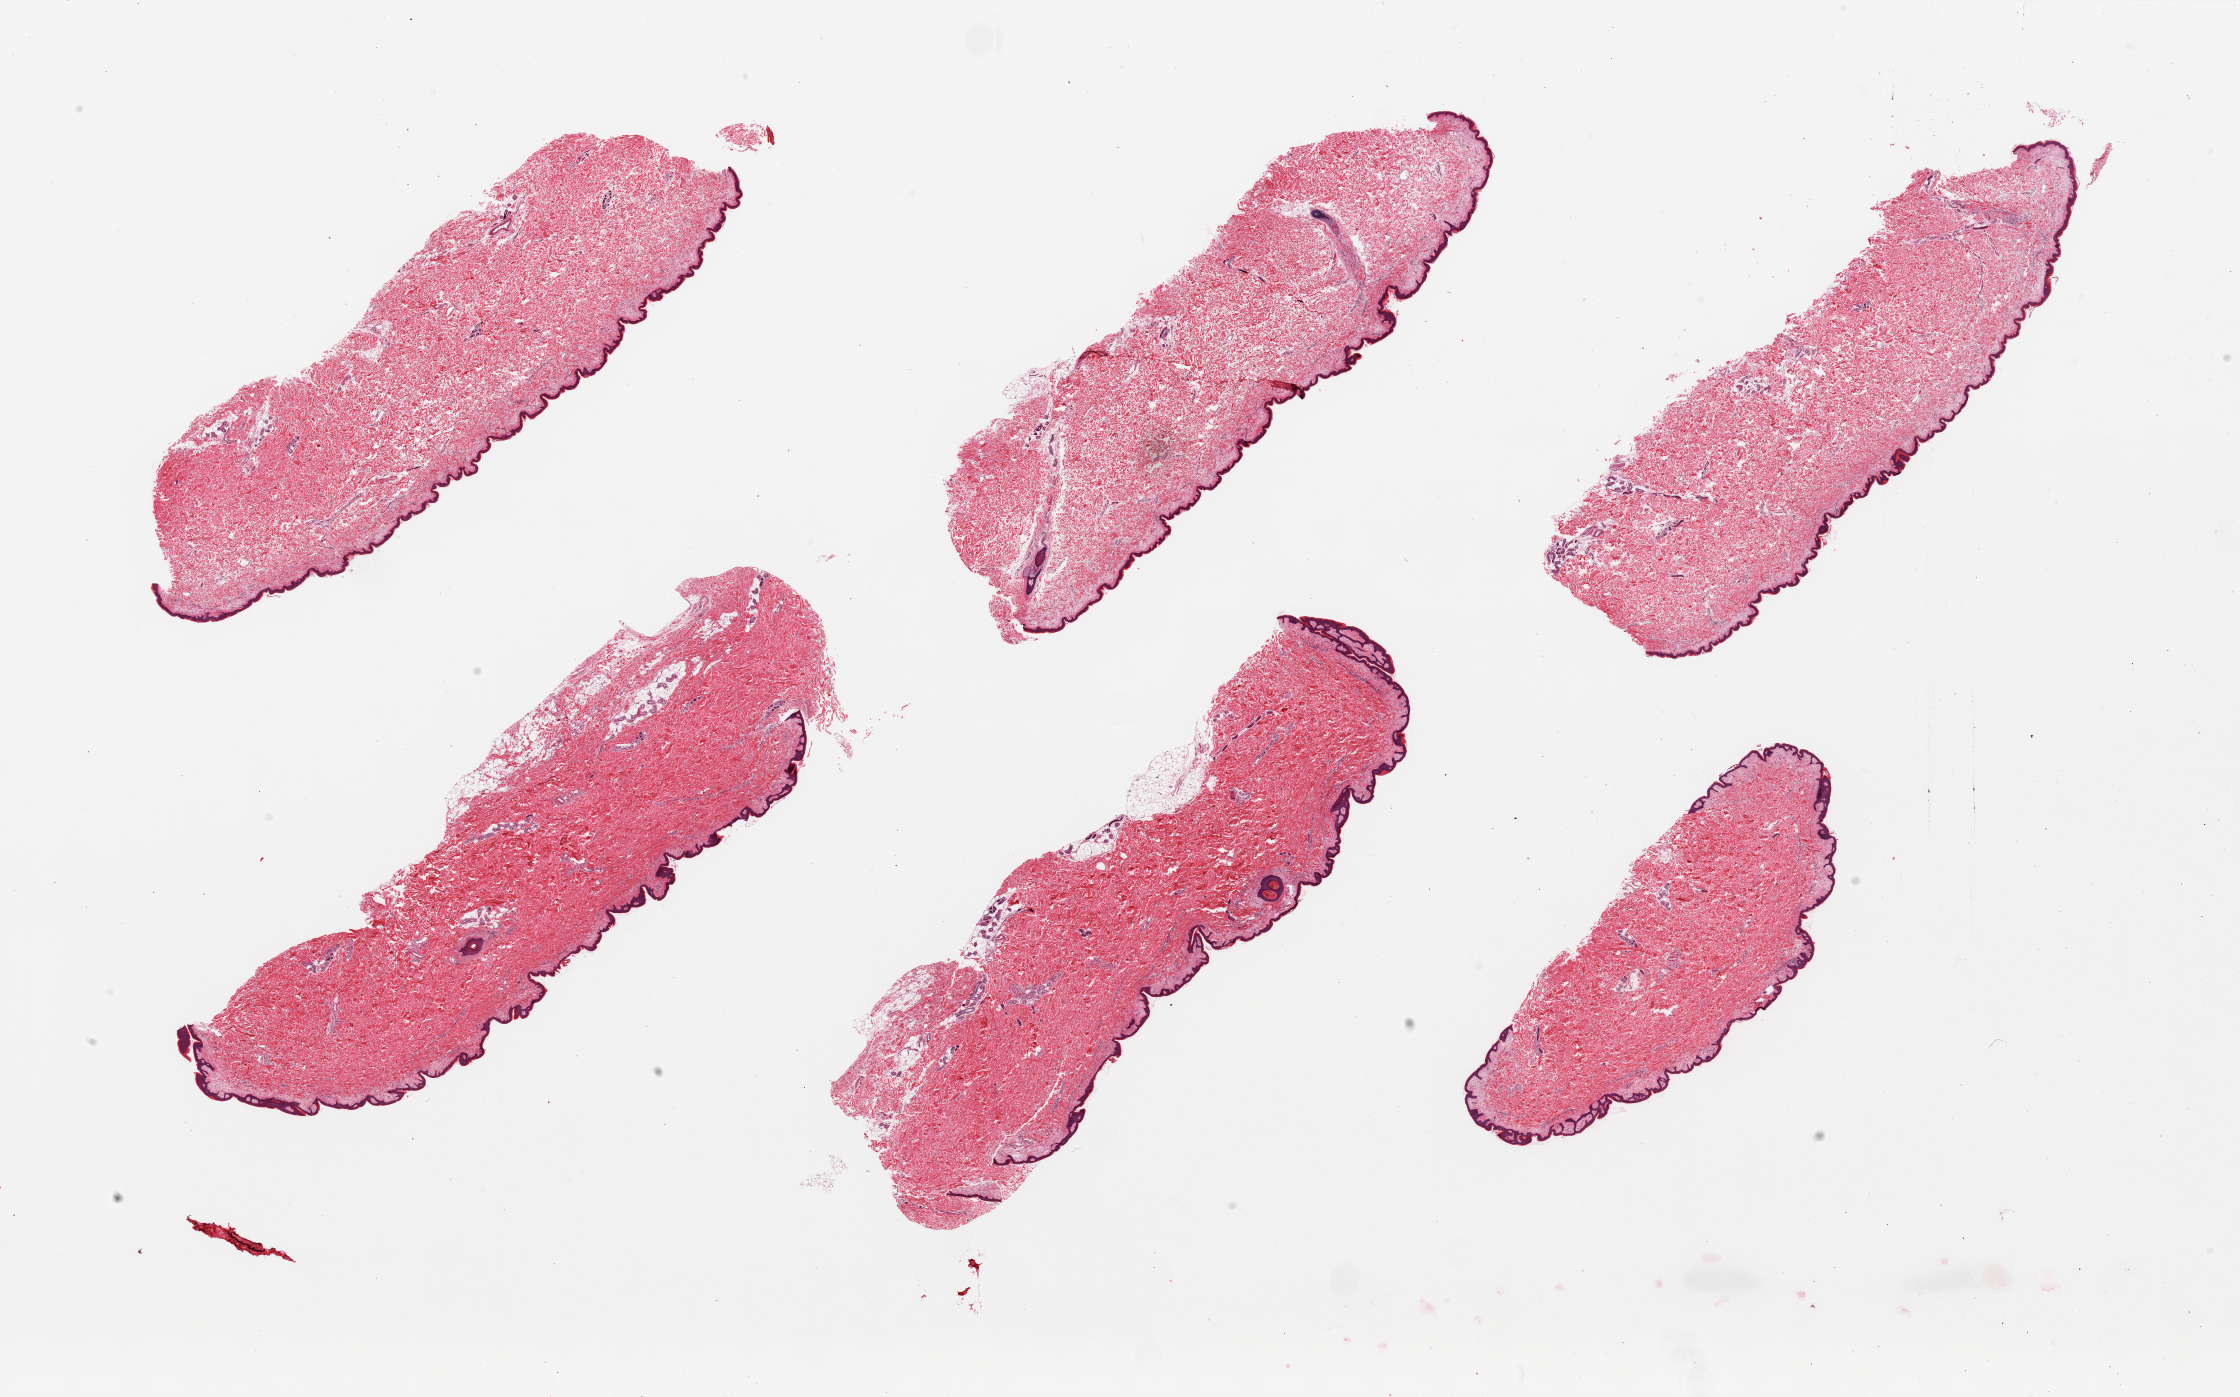
Digitized haematoxylin and eosin-stained section — whole scanned area (about 35.4 x 22.1 mm) shown as a low-resolution overview; PAXgene-fixed, paraffin-embedded tissue; sampled site (target tissue): skin of suprapubic region; tissue donor sample. Male donor.
Review note (as recorded): 6 pieces; well trimmed; 5% intradermal fat.